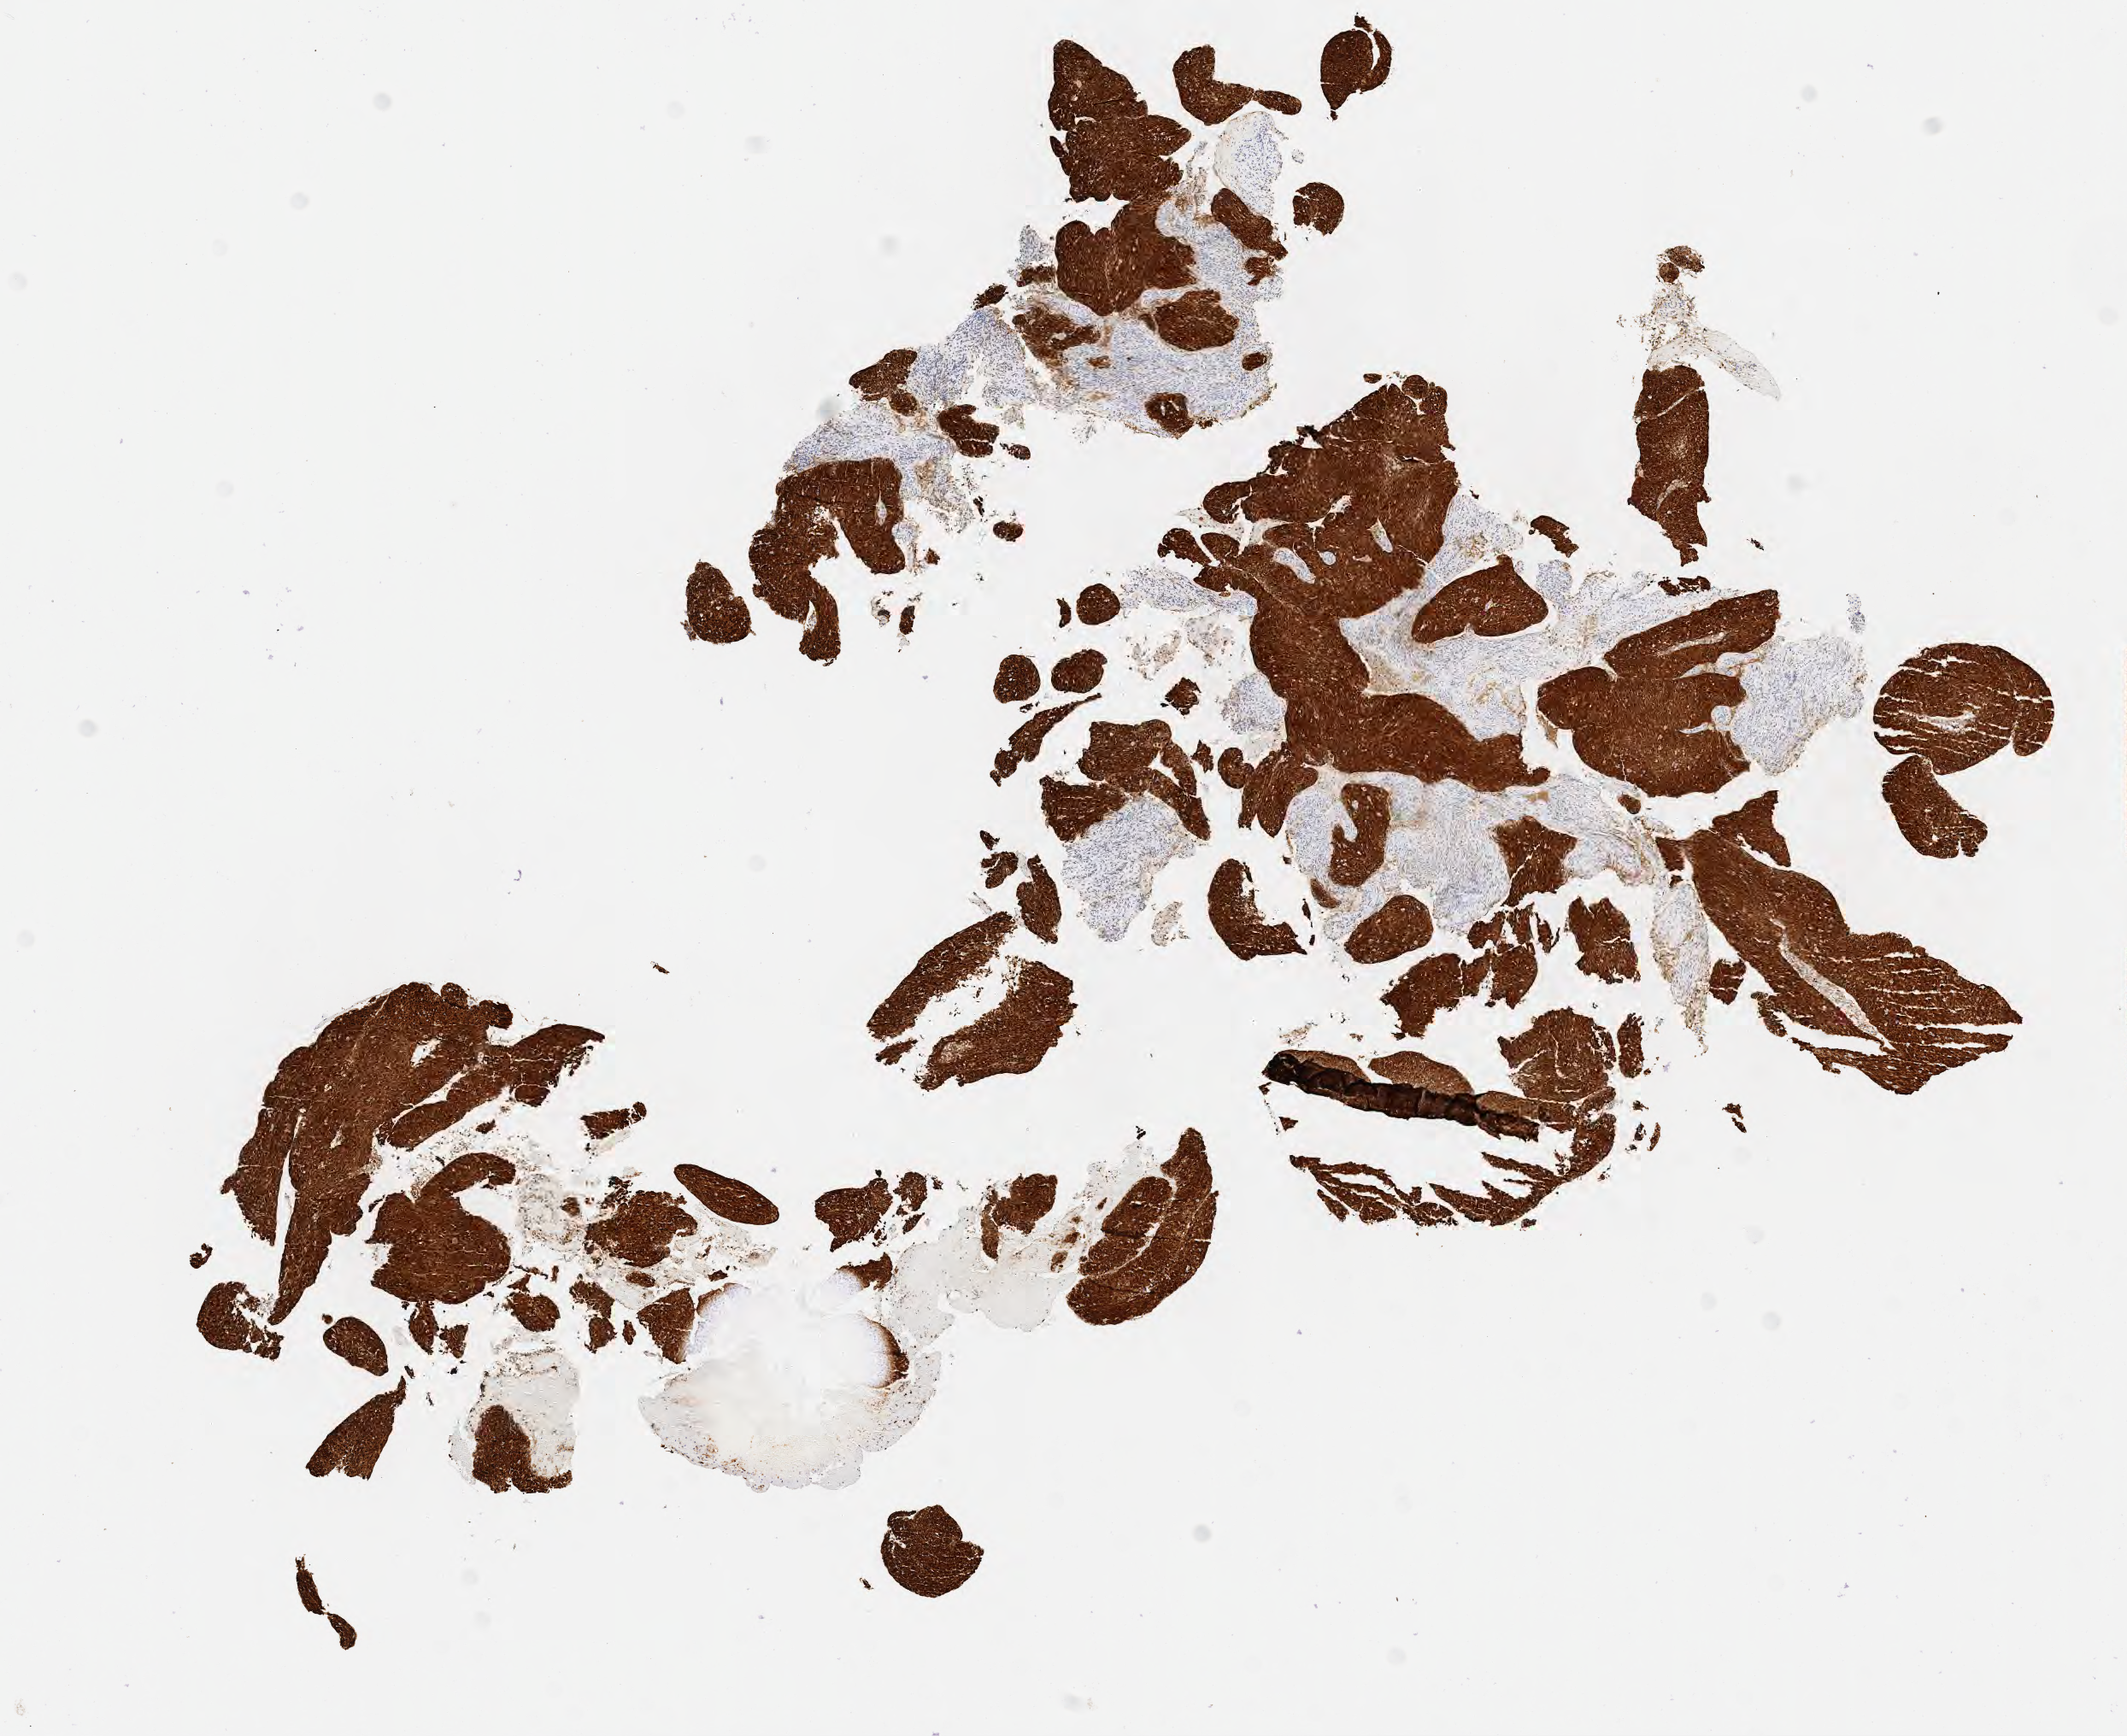
Whole-slide image, immunohistochemical stain for p16 (p16INK4a) — whole scanned area (about 10.1 x 8.2 mm) shown as a low-resolution overview, tumor tissue, site: cervix. Patient: female, age 53 years.
- diagnosis: Squamous cell carcinoma, large cell, nonkeratinizing, NOS